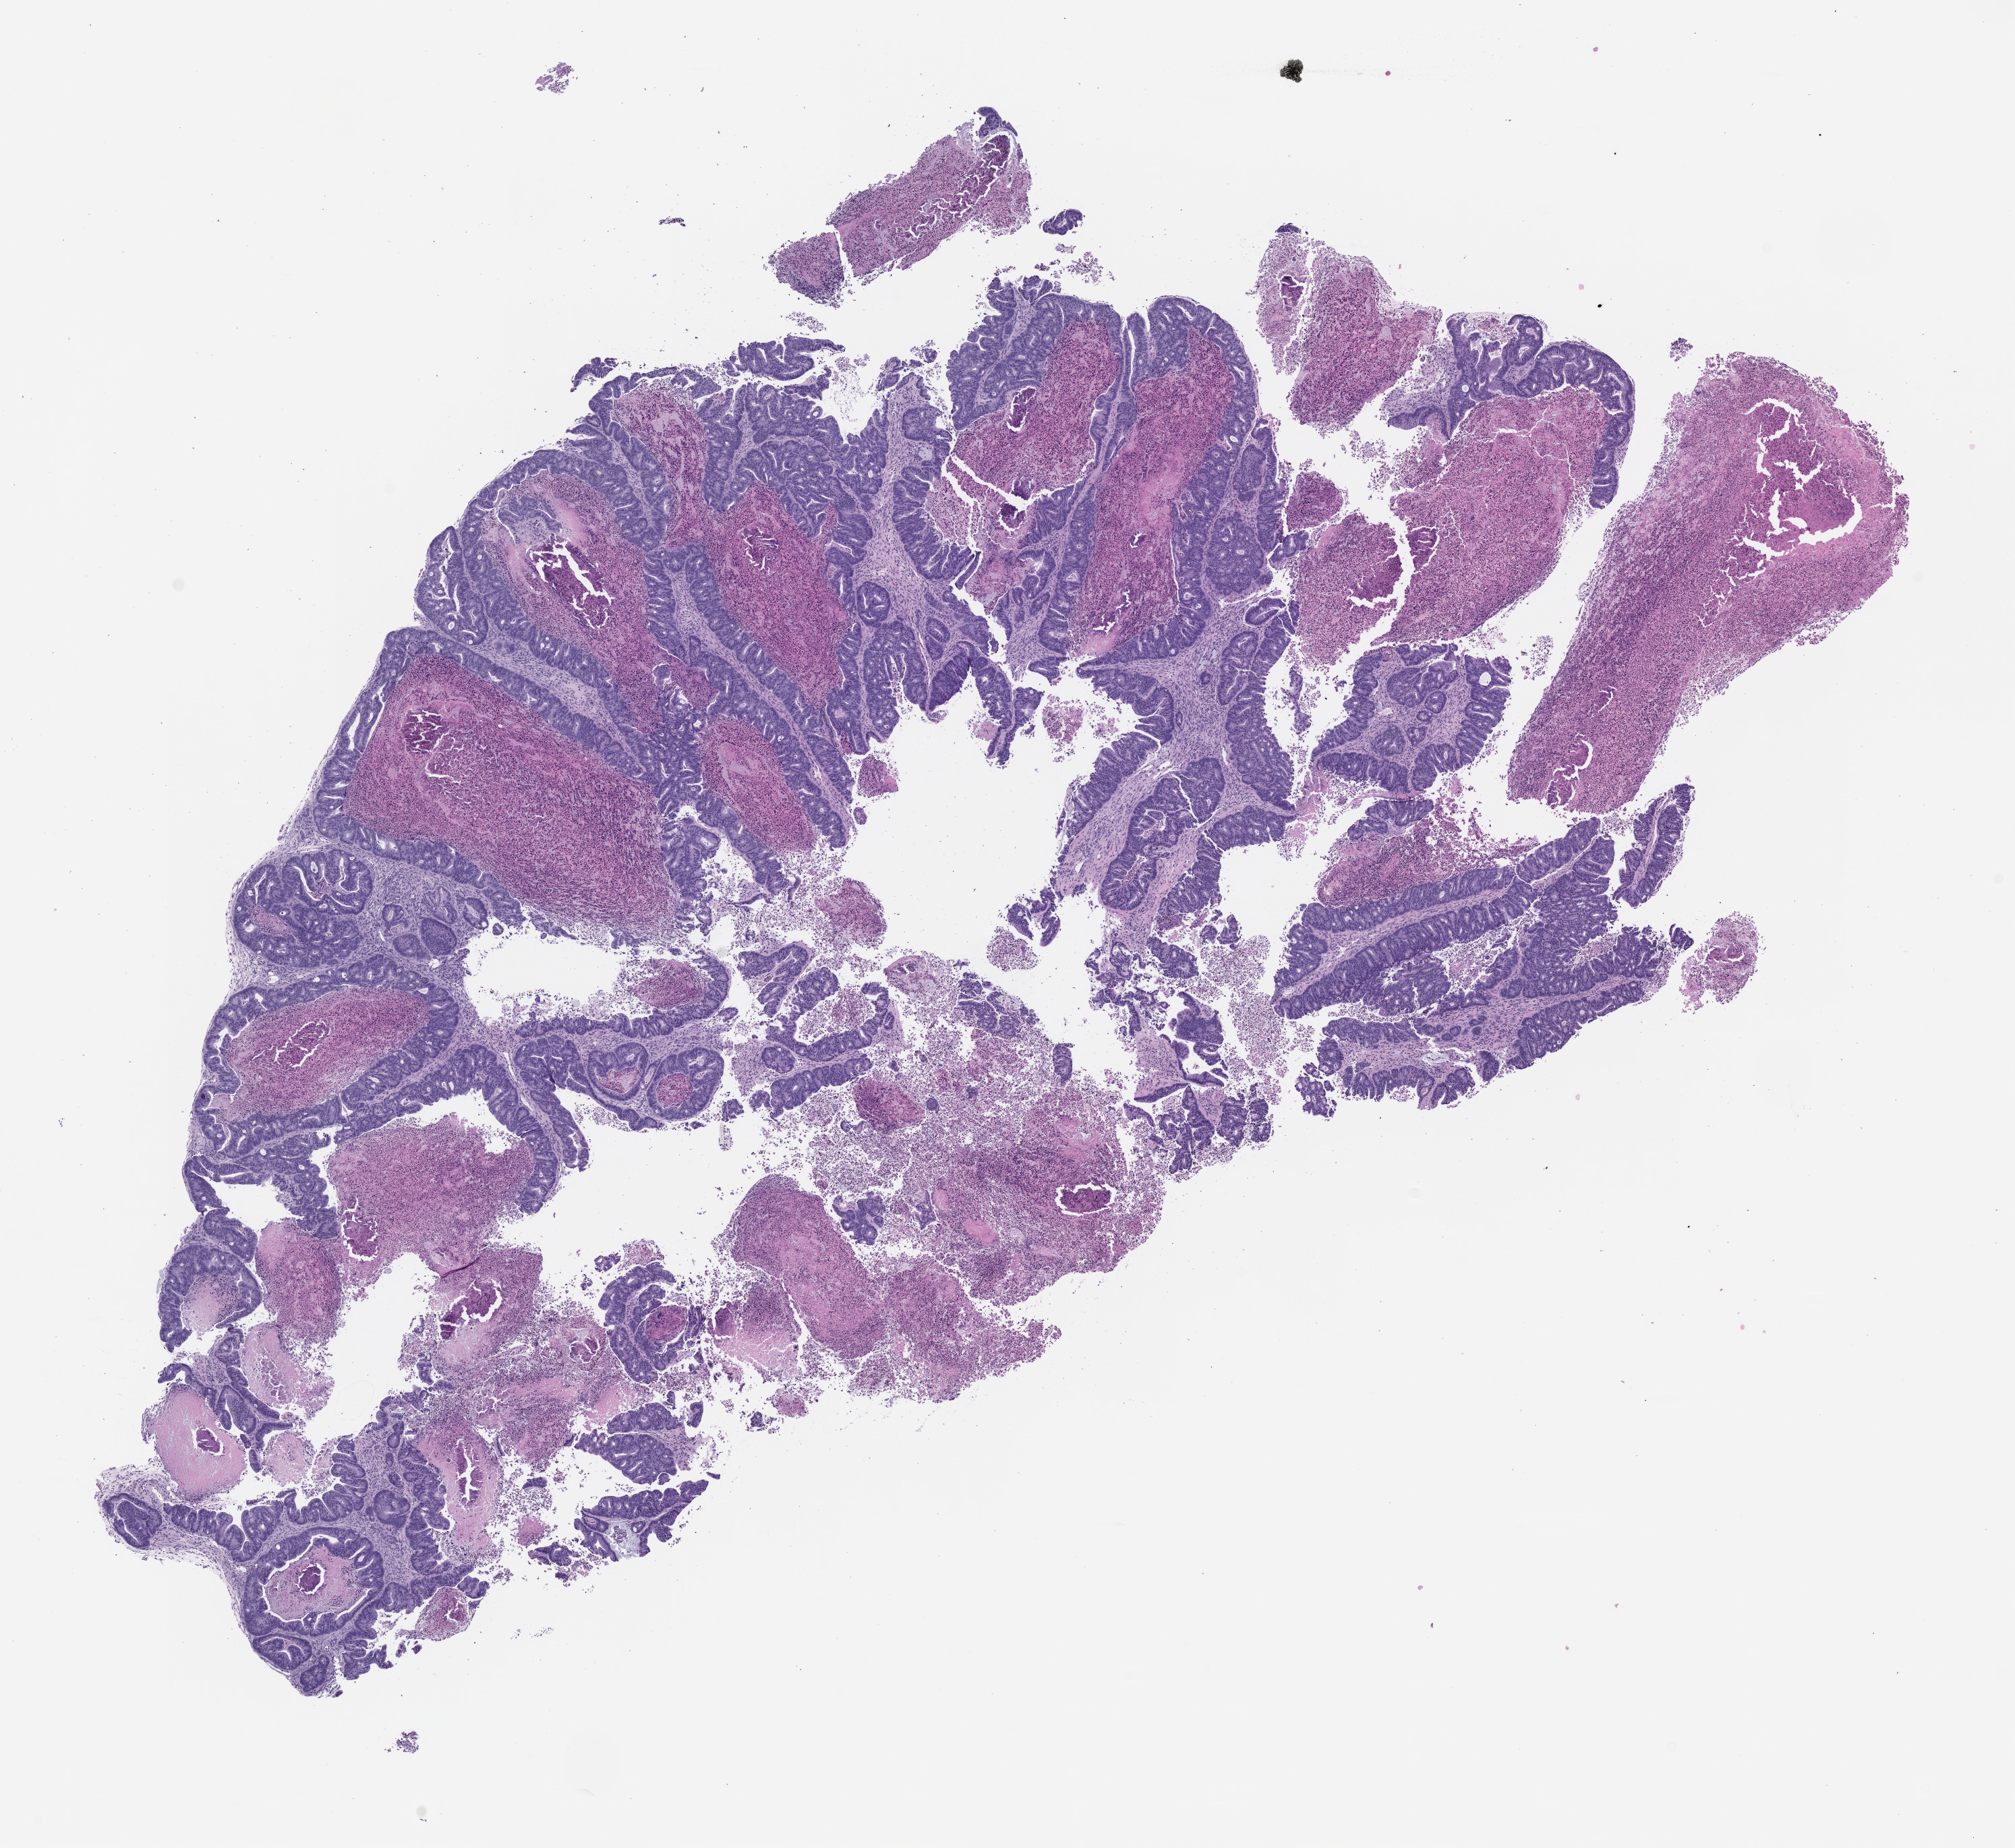
Whole-slide image, H&E: patient-derived xenograft (human tumor grown in a mouse), passage 1, shown as a low-resolution overview of the whole scanned area (about 12.0 x 11.0 mm); formalin-fixed paraffin-embedded section; originating tumor site category: rectum.
* originating patient diagnosis: Rectal Adenocarcinoma